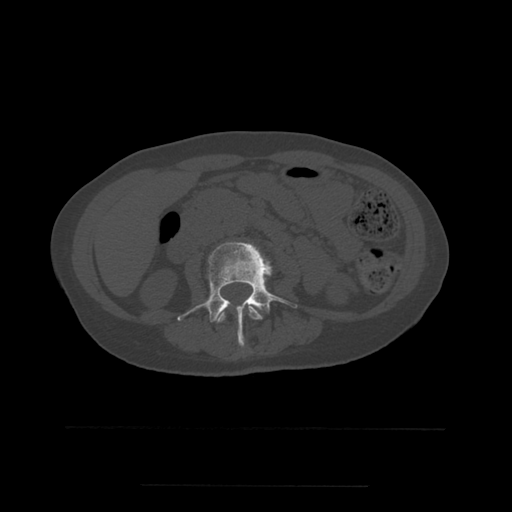
CT including the spine, one axial slice. Position 194 of 544 along the scan axis. Bone window (W 1800 / L 400 HU). 1.25 mm slice thickness. 512 × 512 image matrix, field of view 350 × 350 mm. Patient age 58 years. From the clinical record (not read from this slice): primary cancer: lung.
Outlined on this slice (semi-automatically segmented with operator editing):
- L2 vertebra: box from (x=218, y=305) to (x=263, y=323) px
- L3 vertebra: (x=178, y=242)–(x=298, y=346)